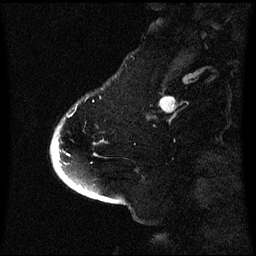
Breast MRI (dynamic contrast-enhanced), one sagittal slice. Position 13 of 60 along the scan axis. Dynamic contrast-enhanced series, image 2 of 3 at this slice position (ordered by acquisition). 1.5 T. TE 4.2 ms, TR 8.4 ms. 2.1 mm slice thickness. 256 × 256 image matrix, field of view 220 × 220 mm. Female patient, age 53 years. From the clinical record (not read from this slice): setting: breast cancer imaged before/during neoadjuvant chemotherapy; receptor status: HR-positive, HER2-negative.
Structures marked on this image (semi-automatically segmented with operator editing):
- analysis volume of interest (the breast-tissue region the enhancement analysis was run in; not a lesion): bounding box <52,124,105,171> (left, top, right, bottom; pixels)
- tumour enhancement mask (voxels above the 70 % enhancement threshold inside the analysis volume of interest): <57,150,70,159>